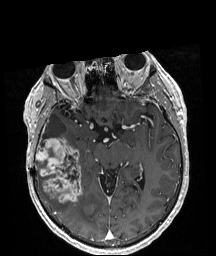
Brain MRI from a brain-tumour surgery series, one axial slice; position 117 of 208 along the scan axis; T1-weighted post-contrast; 1 mm slice thickness; 216 × 256 image matrix, field of view 211 × 250 mm. Case-level facts recorded for this patient, not image findings: histopathology: Astrocytoma; WHO grade: 4; IDH mutation: yes; tumour location: Right Temporal.
Outlined on this slice (expert manual segmentation):
- tumour: bounding box <36,137,82,202> (left, top, right, bottom; pixels)